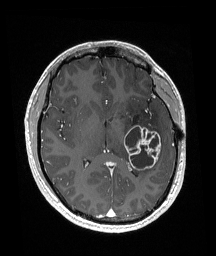
Brain MRI from a brain-tumour surgery series, one axial slice. Slice 92 of 192 in the series (ordered by position). T1-weighted post-contrast. 216 × 256 image matrix, field of view 211 × 250 mm. From the clinical record (not read from this slice): histopathology: Glioneuronal tumor; WHO grade: 2; tumour location: Left Superior Temporal Gyrus.
Outlined on this slice (outlined manually by an expert reader):
- tumour: box from (x=124, y=125) to (x=162, y=171) px